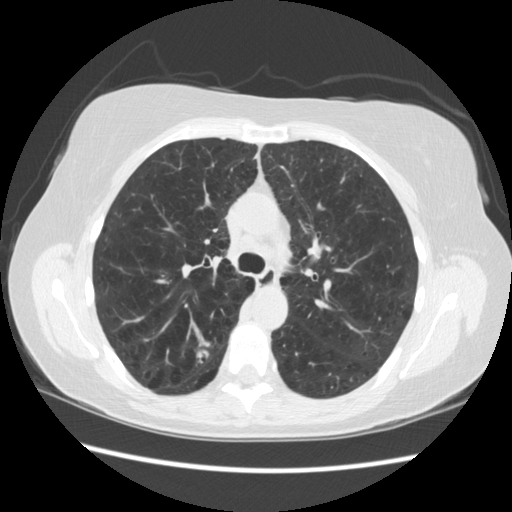
Low-dose screening chest CT, one axial slice; position 156 of 235 along the scan axis; reconstruction kernel STANDARD; lung window (W 1500 / L -600 HU); 2.5 mm slice thickness; 512 × 512 image matrix, field of view 360 × 360 mm.
Structures marked on this image (expert manual segmentation):
- lesion 1 (tumor, upper lobe of right lung): box from (x=196, y=350) to (x=208, y=363) px